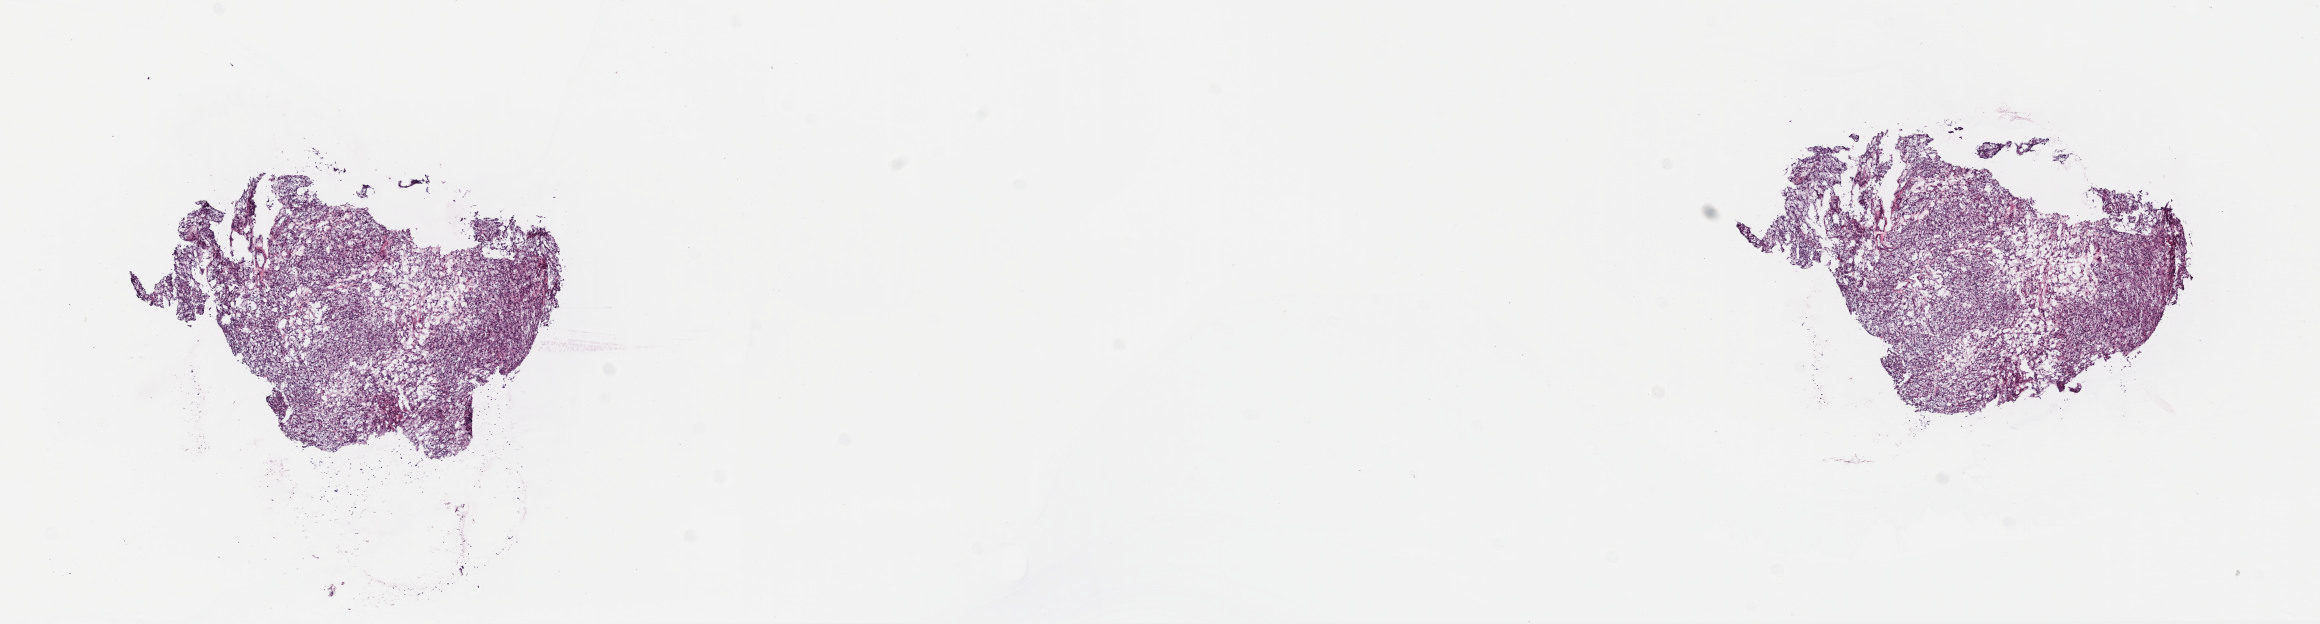
Digitized H&E tissue section (whole slide) — whole scanned area (about 18.2 x 4.9 mm) shown as a low-resolution overview, frozen section, primary tumour sample from the kidney. Male, age 60 years at initial diagnosis. Histologic grade: G2 (moderately differentiated). Pathologist review of this section (percent, as recorded): tumour cells 100%, tumour nuclei 95%, normal cells 0%, stromal cells 0%, necrosis 0%. Infiltration values recorded for this section: lymphocyte infiltration 0%, monocyte infiltration 0%, neutrophil infiltration 0%.
- diagnosis: Renal cell carcinoma, NOS
- AJCC pathologic stage: II (7th edition)
- laterality: right
- TNM: T2a NX MX